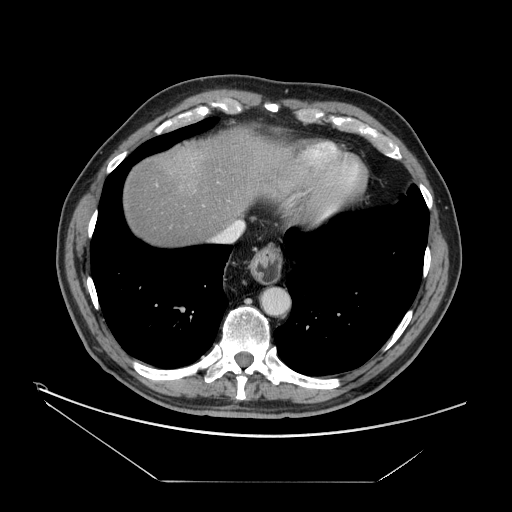
Contrast-enhanced abdominal CT, one axial slice; slice 144 of 161 in the series (ordered by position); intravenous contrast given; soft-tissue window (W 400 / L 40 HU); 2.5 mm slice thickness; 512 × 512 image matrix, field of view 440 × 440 mm. Male patient, age 65 years. Case-level facts recorded for this patient, not image findings: diagnosis: colorectal cancer liver metastases, imaged before liver resection; multiple liver metastases: yes; largest metastasis: 4.2 cm; disease in both lobes: yes.
Structures marked on this image (expert manual segmentation):
- hepatic veins: bounding box <217,221,244,242> (left, top, right, bottom; pixels)
- liver: <123,128,291,246>
- planned liver remnant (the part of the liver to remain after resection): <123,128,292,246>